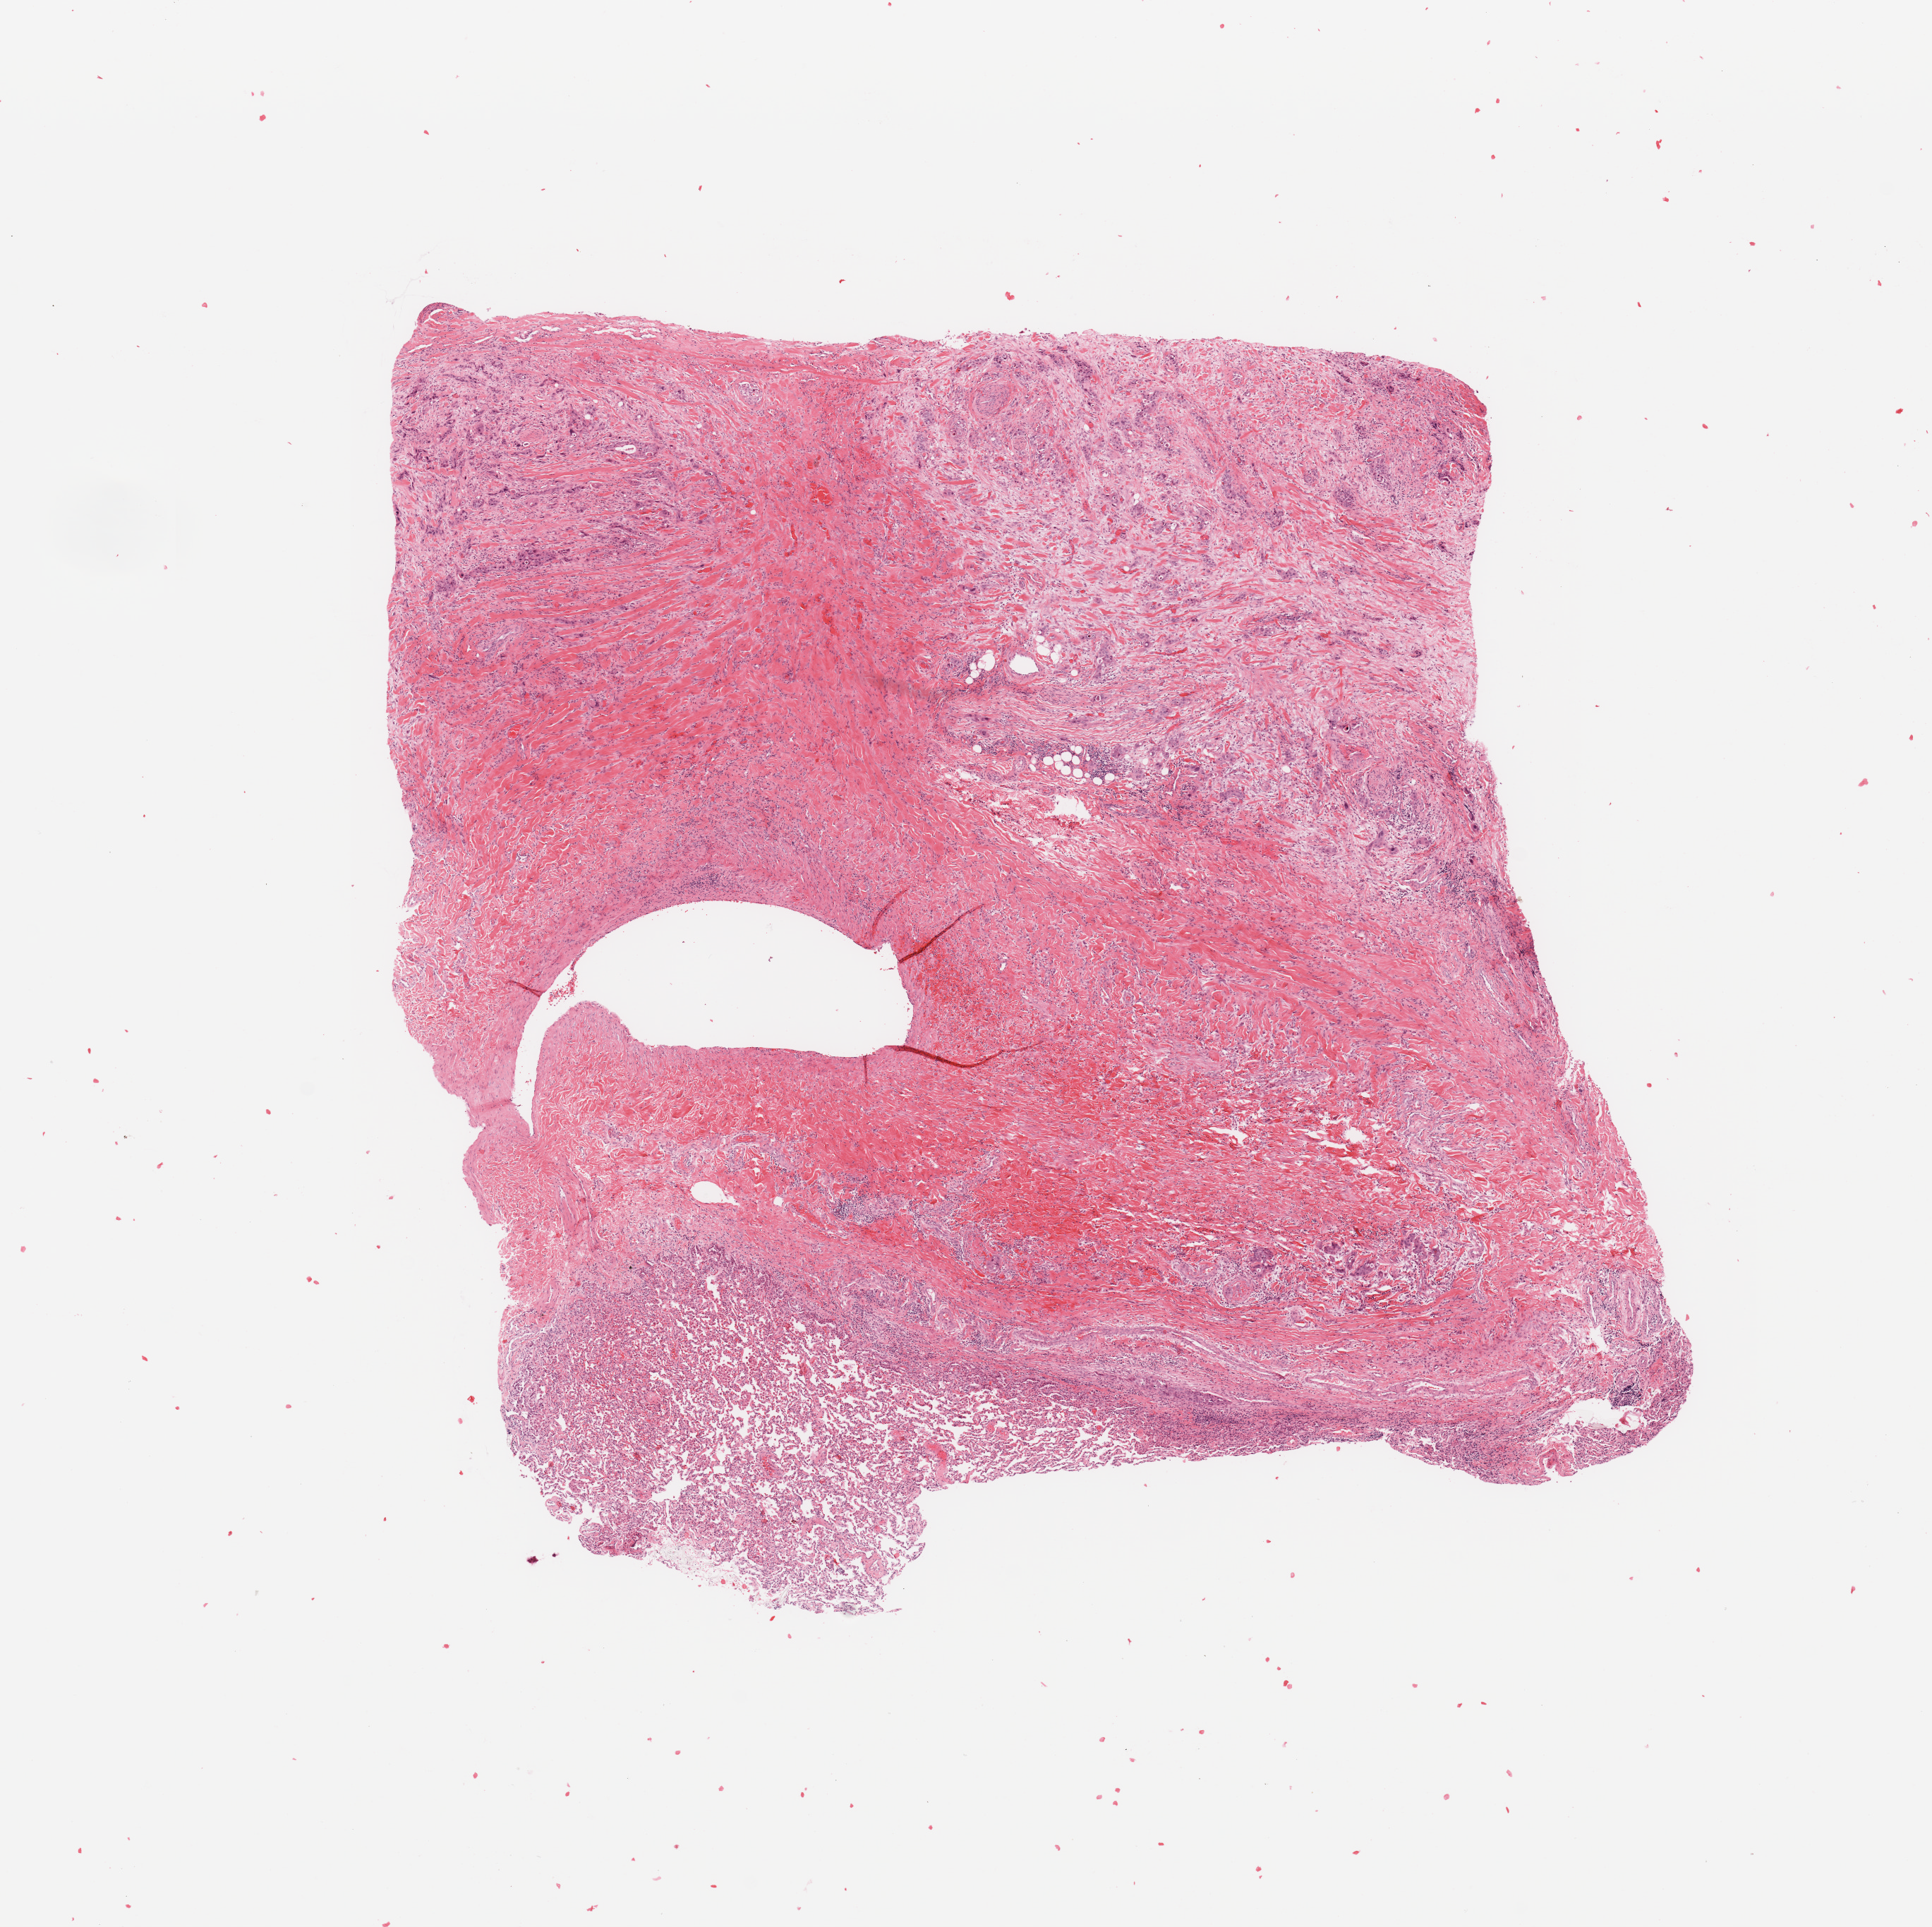
Digitized H&E tissue section (whole slide), a low-resolution overview of the entire scanned area, about 10.8 x 10.8 mm (acquisition: 20x scan), lung, tumour tissue. 40-year-old male patient. Histologic grade: G3 (poorly differentiated).
AJCC pathologic stage: IIIA. Histologic diagnosis: Squamous cell carcinoma, NOS. Primary tumour site (as recorded): right middle lobe.